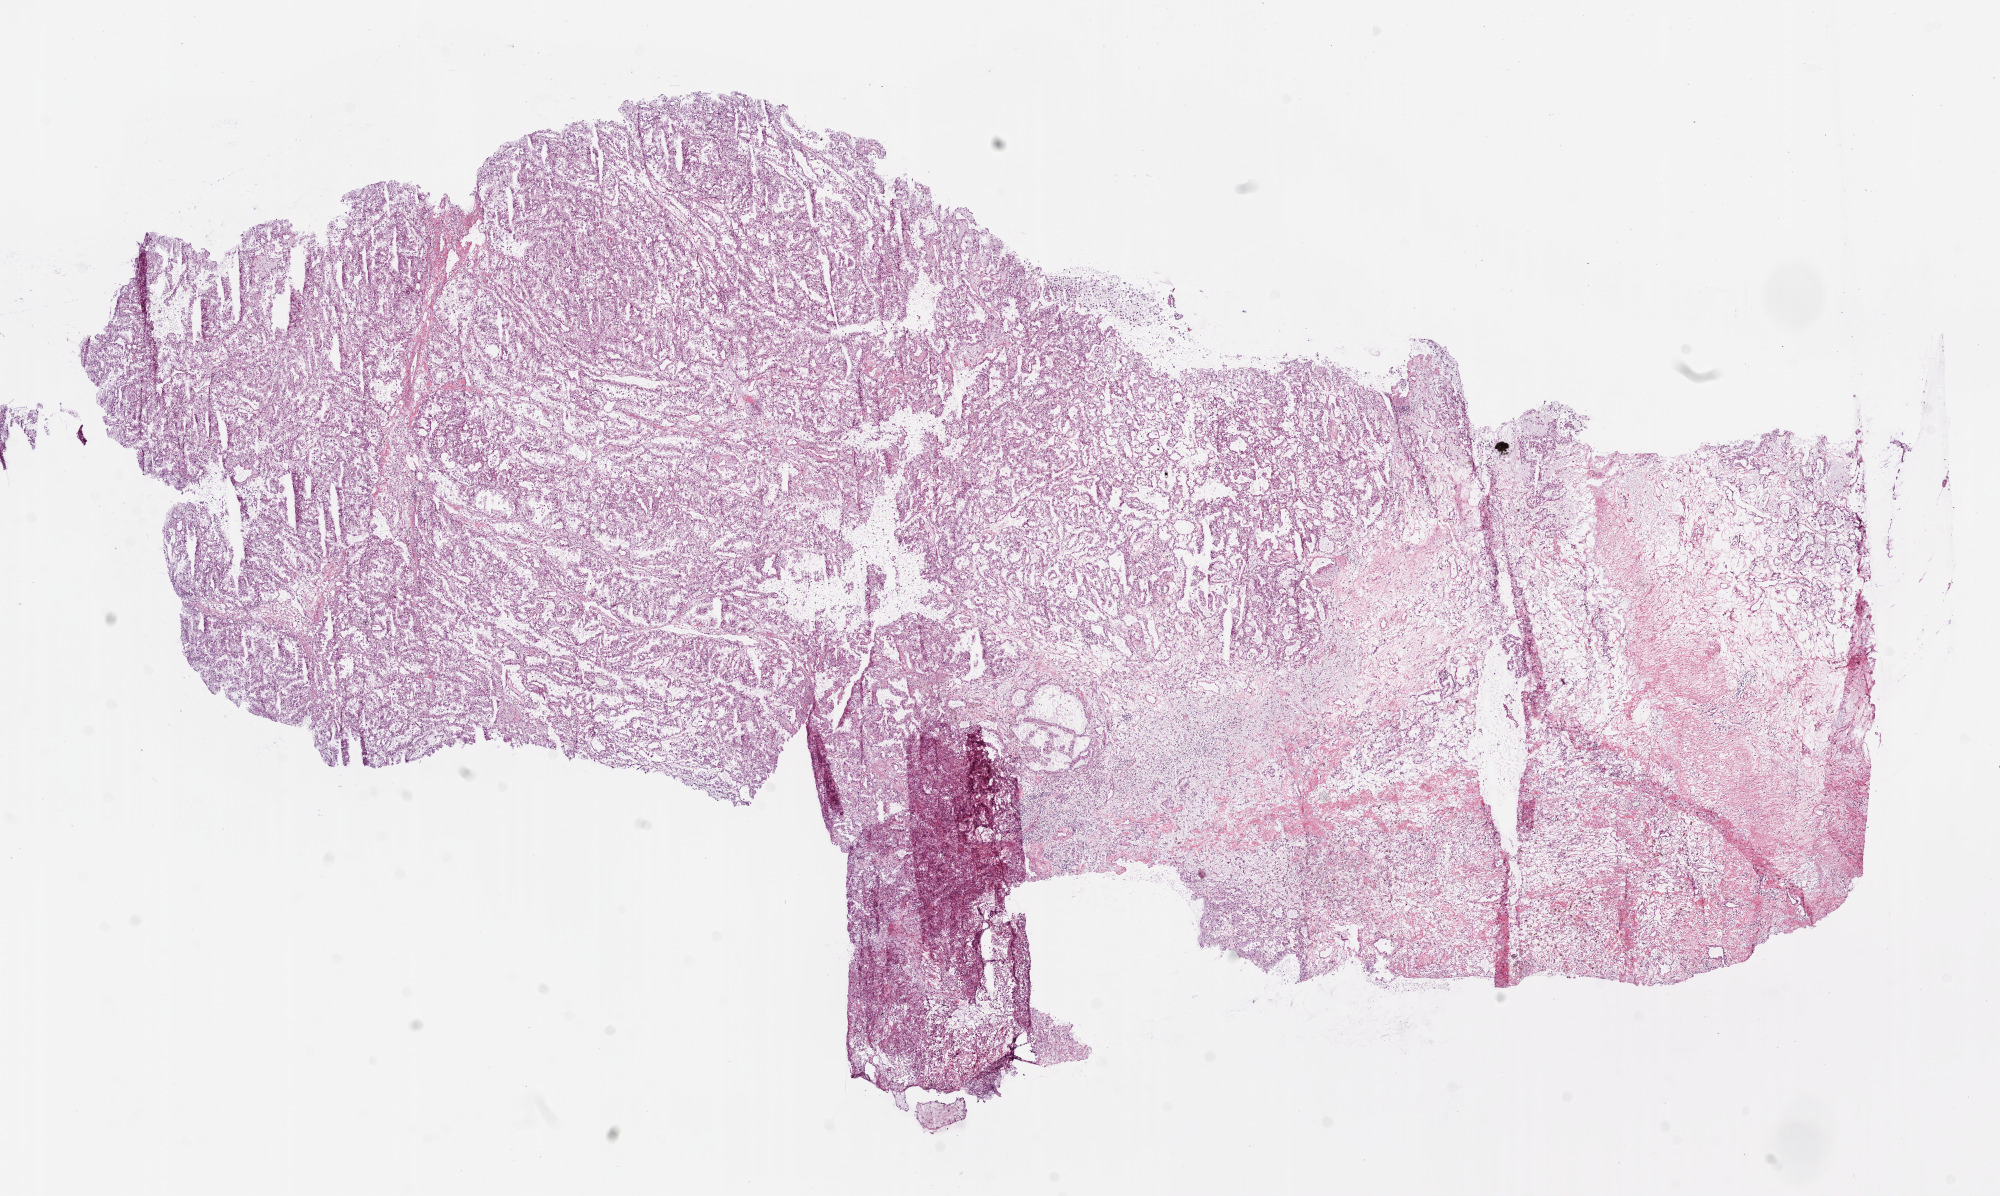
H&E whole-slide image — shown as a low-resolution overview of the whole scanned area (about 16.0 x 9.6 mm); frozen section from the bottom of the tissue portion; sample: primary tumour, kidney. Patient: male, age at initial diagnosis 49 years. Histologic grade: G3 (poorly differentiated). Slide review estimates, as recorded: tumour cells 80%, tumour nuclei 80%, normal cells 0%, stromal cells 20%, necrosis 0%.
* AJCC pathologic stage: I
* diagnosis: Clear cell adenocarcinoma, NOS